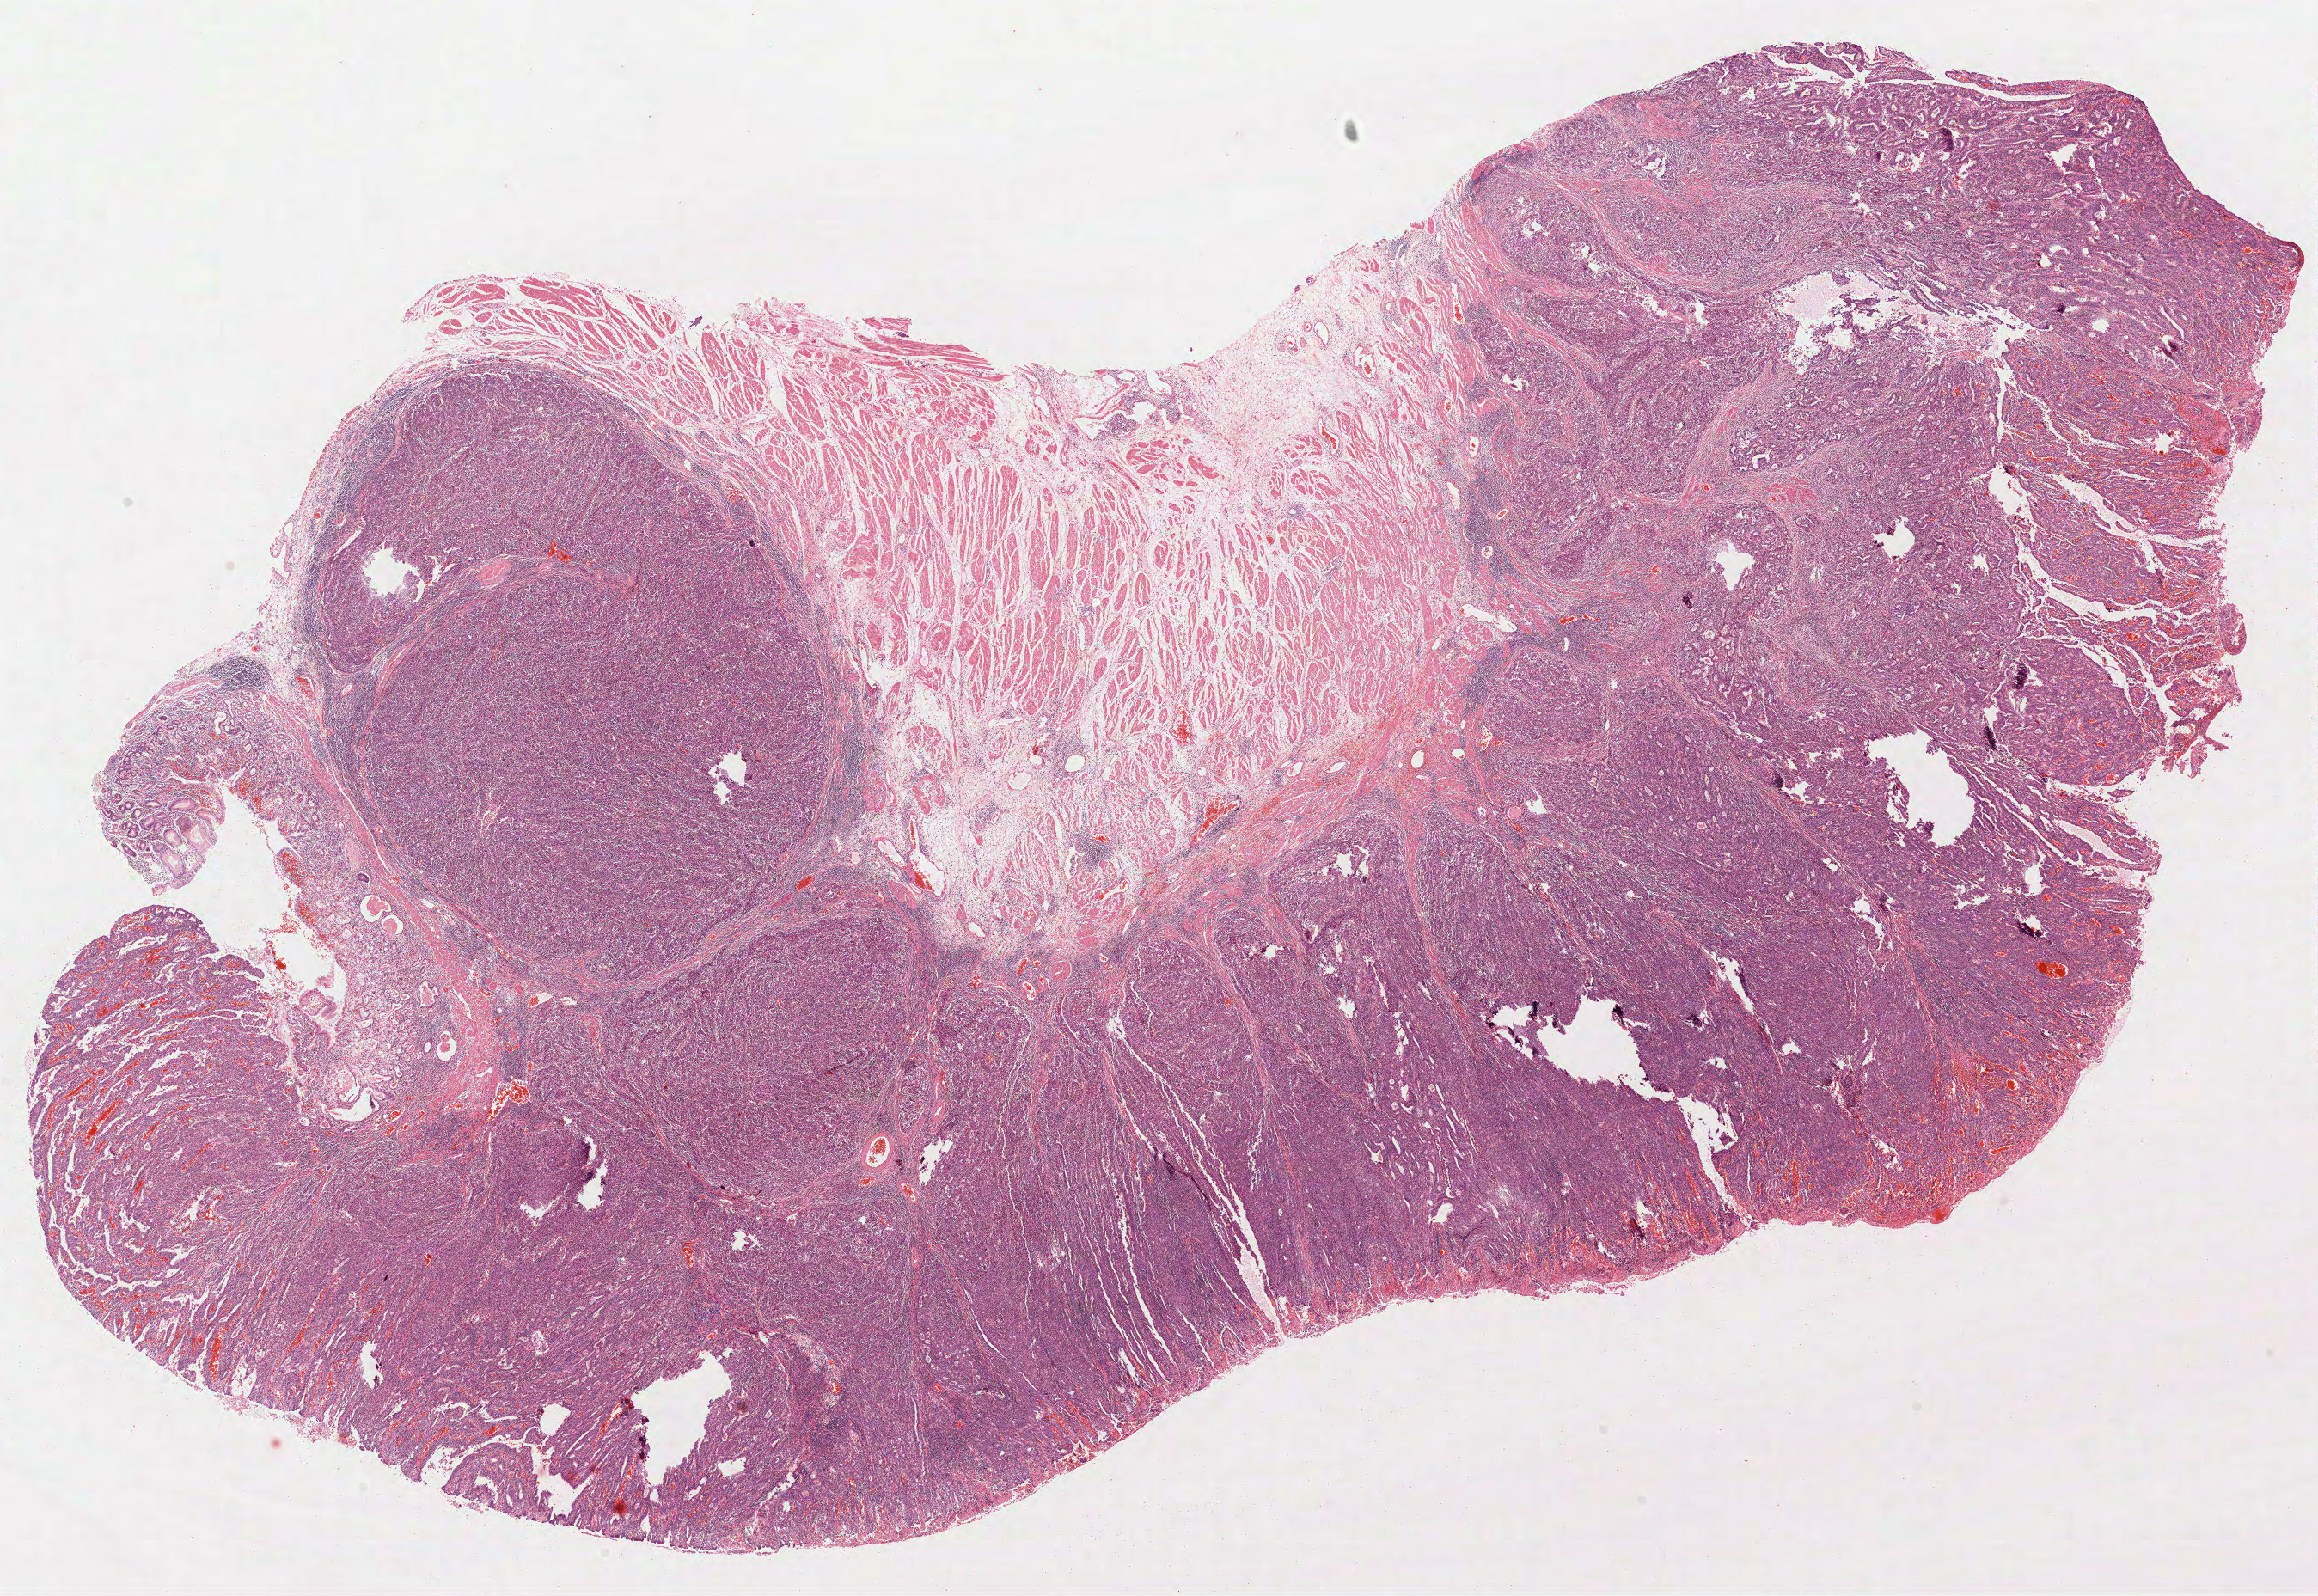
Whole-slide histology image, H&E-stained — whole scanned area (about 21.8 x 15.0 mm, slide scanned at 40x) shown as a low-resolution overview, formalin-fixed paraffin-embedded (FFPE) diagnostic section, primary tumour sample from the stomach. Patient: male, age at initial diagnosis 56 years. Histologic grade: G3 (poorly differentiated).
Pathologic diagnosis: Adenocarcinoma, NOS (fundus of stomach). Lymph nodes positive (case pathology): 1 of 8 examined. AJCC pathologic stage: IIIB (7th edition).